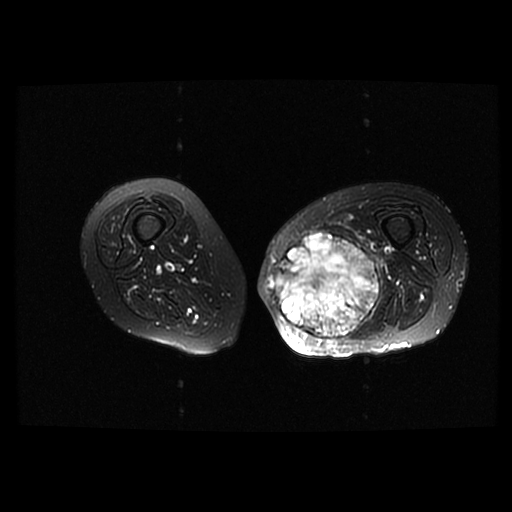
MRI of an extremity soft-tissue mass, one axial slice. Position 29 of 42 along the scan axis. T2-weighted fat-saturated. 512 × 512 image matrix. Female patient. From the clinical record (not read from this slice): histological type: pleomorphic leiomyosarcoma; grade: high; site of the primary tumour: left thigh.
Outlined on this slice (outlined manually by an expert reader):
- gross tumour volume including surrounding oedema: bounding box (x1, y1, x2, y2) in pixels: (264, 231, 382, 340)
- gross tumour volume (mass): (264, 231, 380, 340)